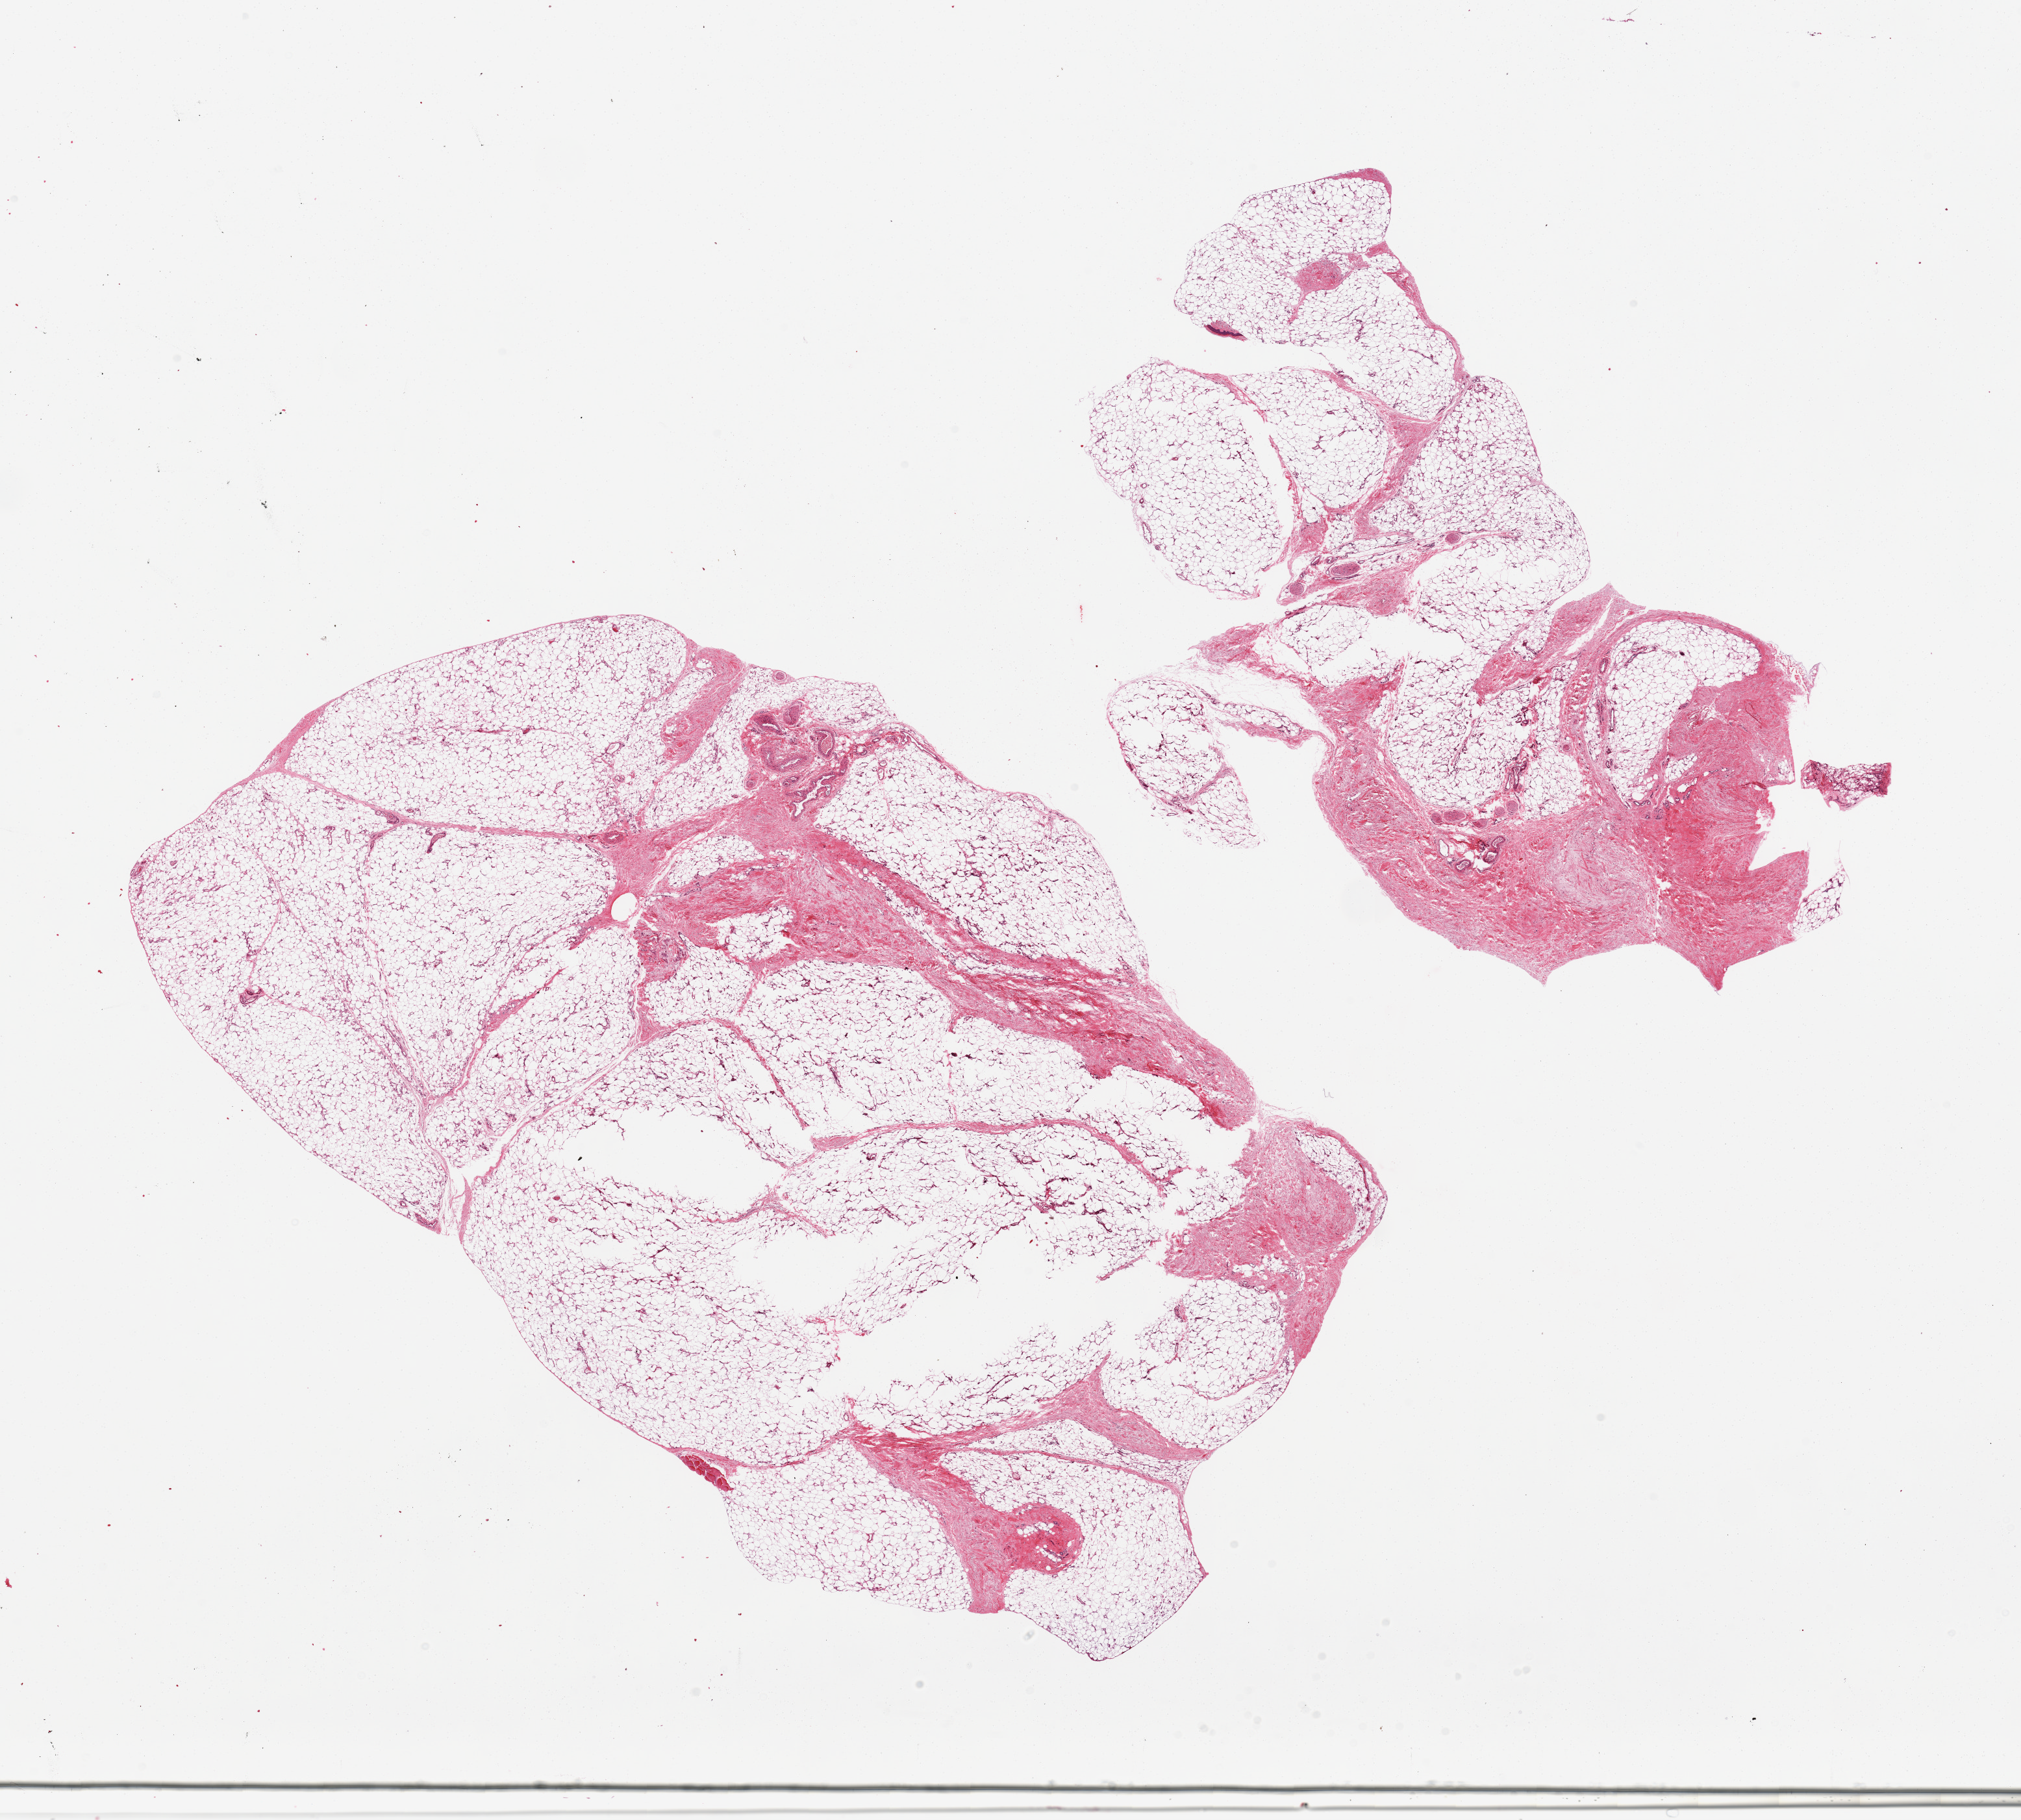
Digitized haematoxylin and eosin-stained section, brightfield, shown as a low-resolution overview of the whole scanned area (about 24.6 x 22.2 mm, acquisition: 20x scan); PAXgene-fixed paraffin-embedded (PFPE) section; sampled site (target tissue): adipose tissue; tissue donor sample. Donor sex: female.
Review note (as recorded): 2 pieces, ~20% fascia/fibrous tissue.